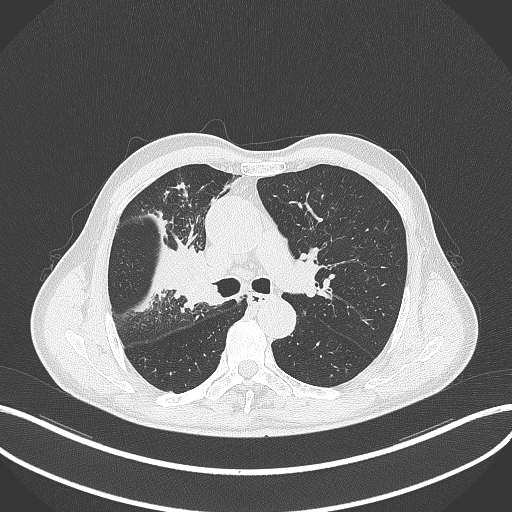
Chest CT, one axial slice; slice 313 of 490 in the series (ordered by position); 120 kVp; lung window (W 1500 / L -600 HU); 512 × 512 image matrix. Male patient, age 69 years. Case-level facts recorded for this patient, not image findings: clinical TNM (as recorded): T2a N0 M0.
Structures marked on this image (rectangle marked by the reading radiologist):
- lung tumour (recorded histology: adenocarcinoma): box from (x=171, y=238) to (x=226, y=314) px